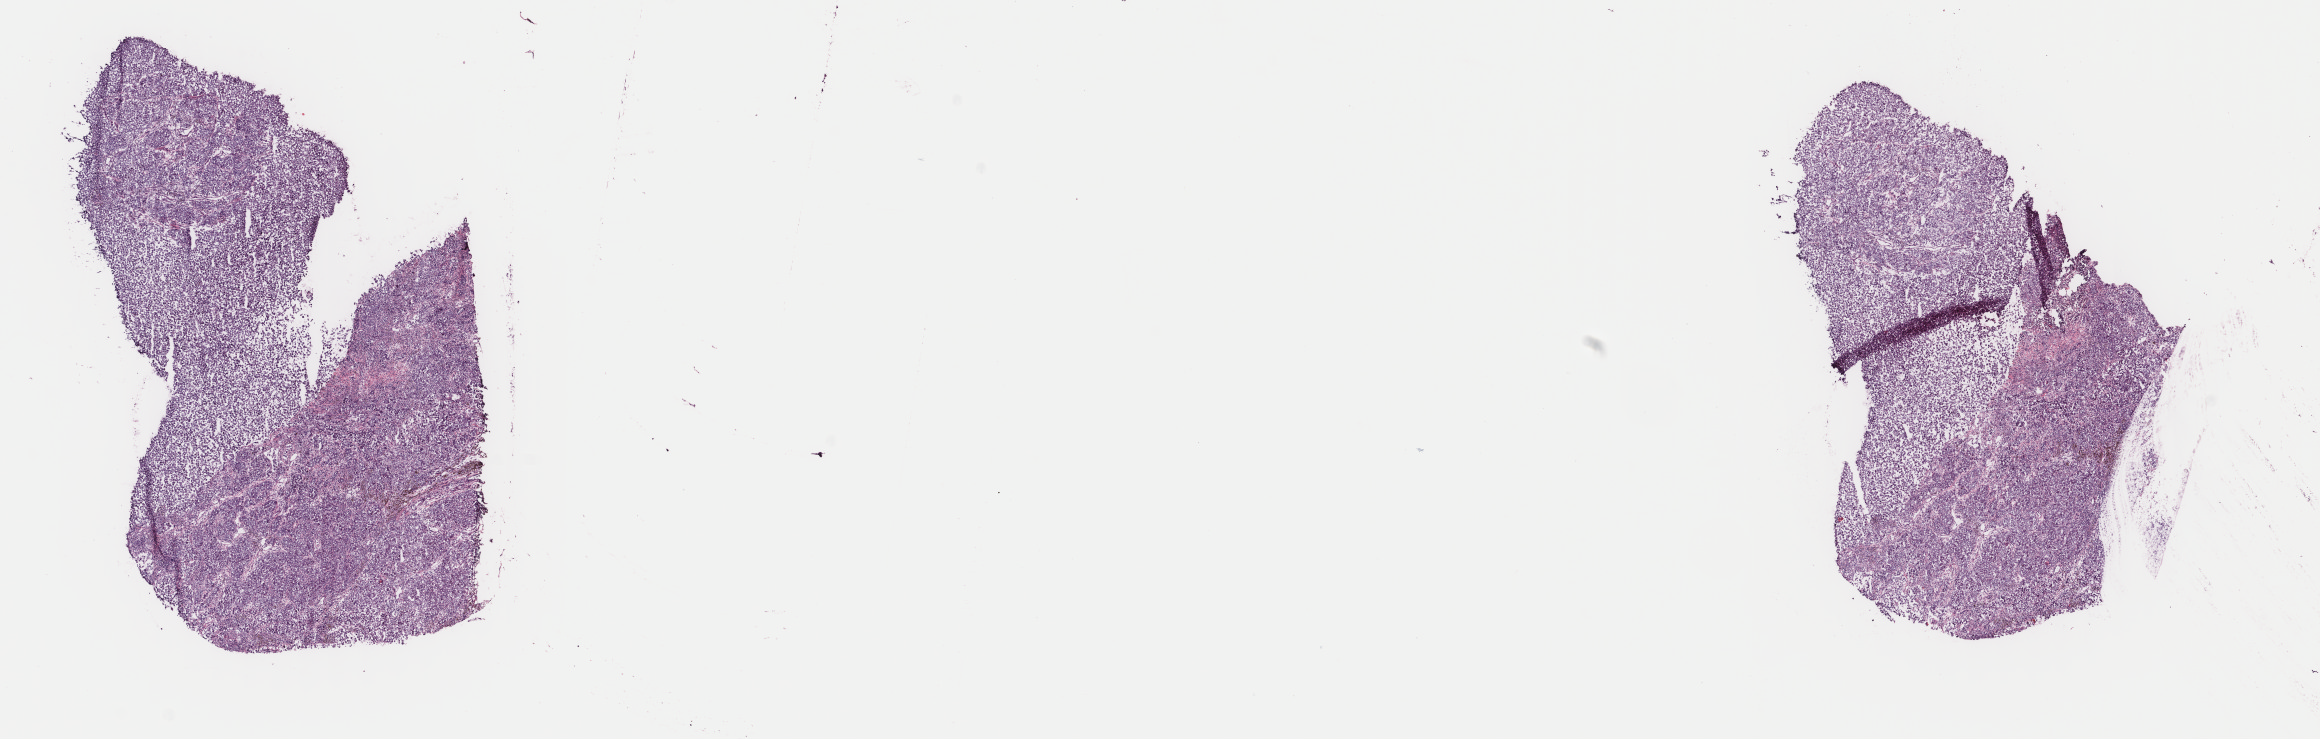
Hematoxylin and eosin (H&E) stained whole-slide image, a low-resolution overview of the entire scanned area, about 18.4 x 5.9 mm (slide scanned at 40x), frozen section from the top of the tissue portion, sample: primary tumour, skin. Patient: female, age at initial diagnosis 54 years. Composition of this section per pathologist review: tumour cells 100%, tumour nuclei 80%, normal cells 0%, stromal cells 0%, necrosis 0%. Infiltration values recorded for this section: lymphocyte infiltration 2%, monocyte infiltration 0%, neutrophil infiltration 0%.
- diagnosis: Superficial spreading melanoma